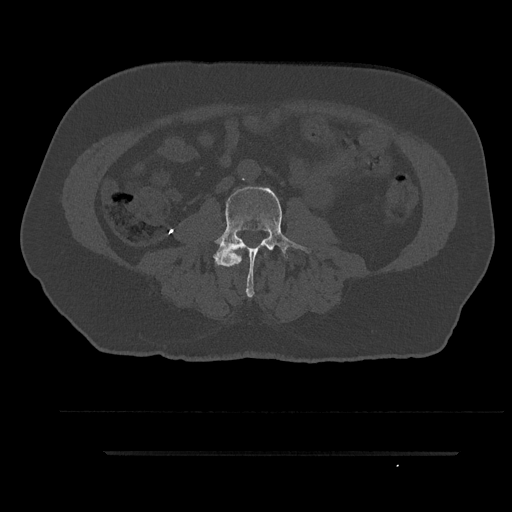
CT including the spine, one axial slice. Slice 41 of 797 in the series (ordered by position). 120 kVp. Bone window (W 1800 / L 400 HU). 0.5 mm slice thickness. 512 × 512 image matrix, field of view 432 × 432 mm. Male patient, age 63 years. From the clinical record (not read from this slice): primary cancer: renal; vertebrae with lytic lesions (as recorded): T8.
Structures marked on this image (semi-automatically segmented with operator editing):
- L2 vertebra: bounding box [x1, y1, x2, y2] px = [235, 250, 267, 264]
- L3 vertebra: [201, 185, 312, 298]